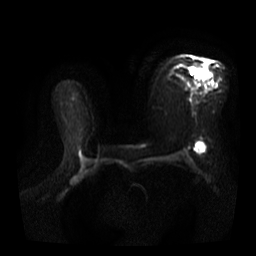
Breast MRI, one axial slice; position 23 of 40 along the scan axis; diffusion-weighted series; image 2 of 4 stored at this slice position (different b-values; order by instance number); 3 T; 5 mm slice thickness; 256 × 256 image matrix, field of view 360 × 360 mm. Female patient.
Outlined on this slice (expert manual segmentation):
- tumour on diffusion-weighted imaging: bounding box <195,63,208,74> (left, top, right, bottom; pixels)